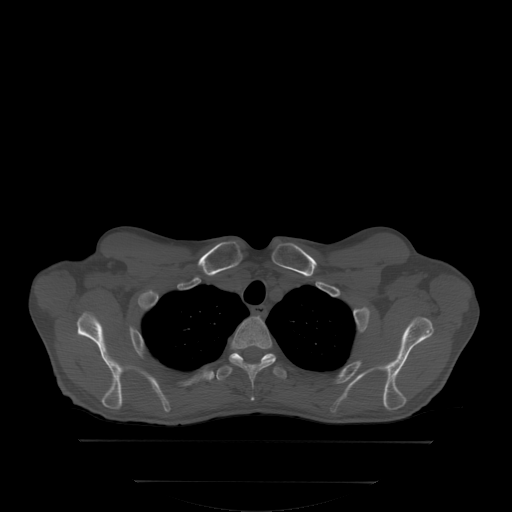
CT including the spine, one axial slice; slice 275 of 350 in the series (ordered by position); bone window (W 1800 / L 400 HU); 512 × 512 image matrix. Patient: male, 58 years. From the clinical record (not read from this slice): primary cancer: prostate.
Outlined on this slice (semi-automatic segmentation, software-assisted and operator-edited):
- T2 vertebra: bounding box <231,316,277,400> (left, top, right, bottom; pixels)
- T3 vertebra: <214,352,287,379>